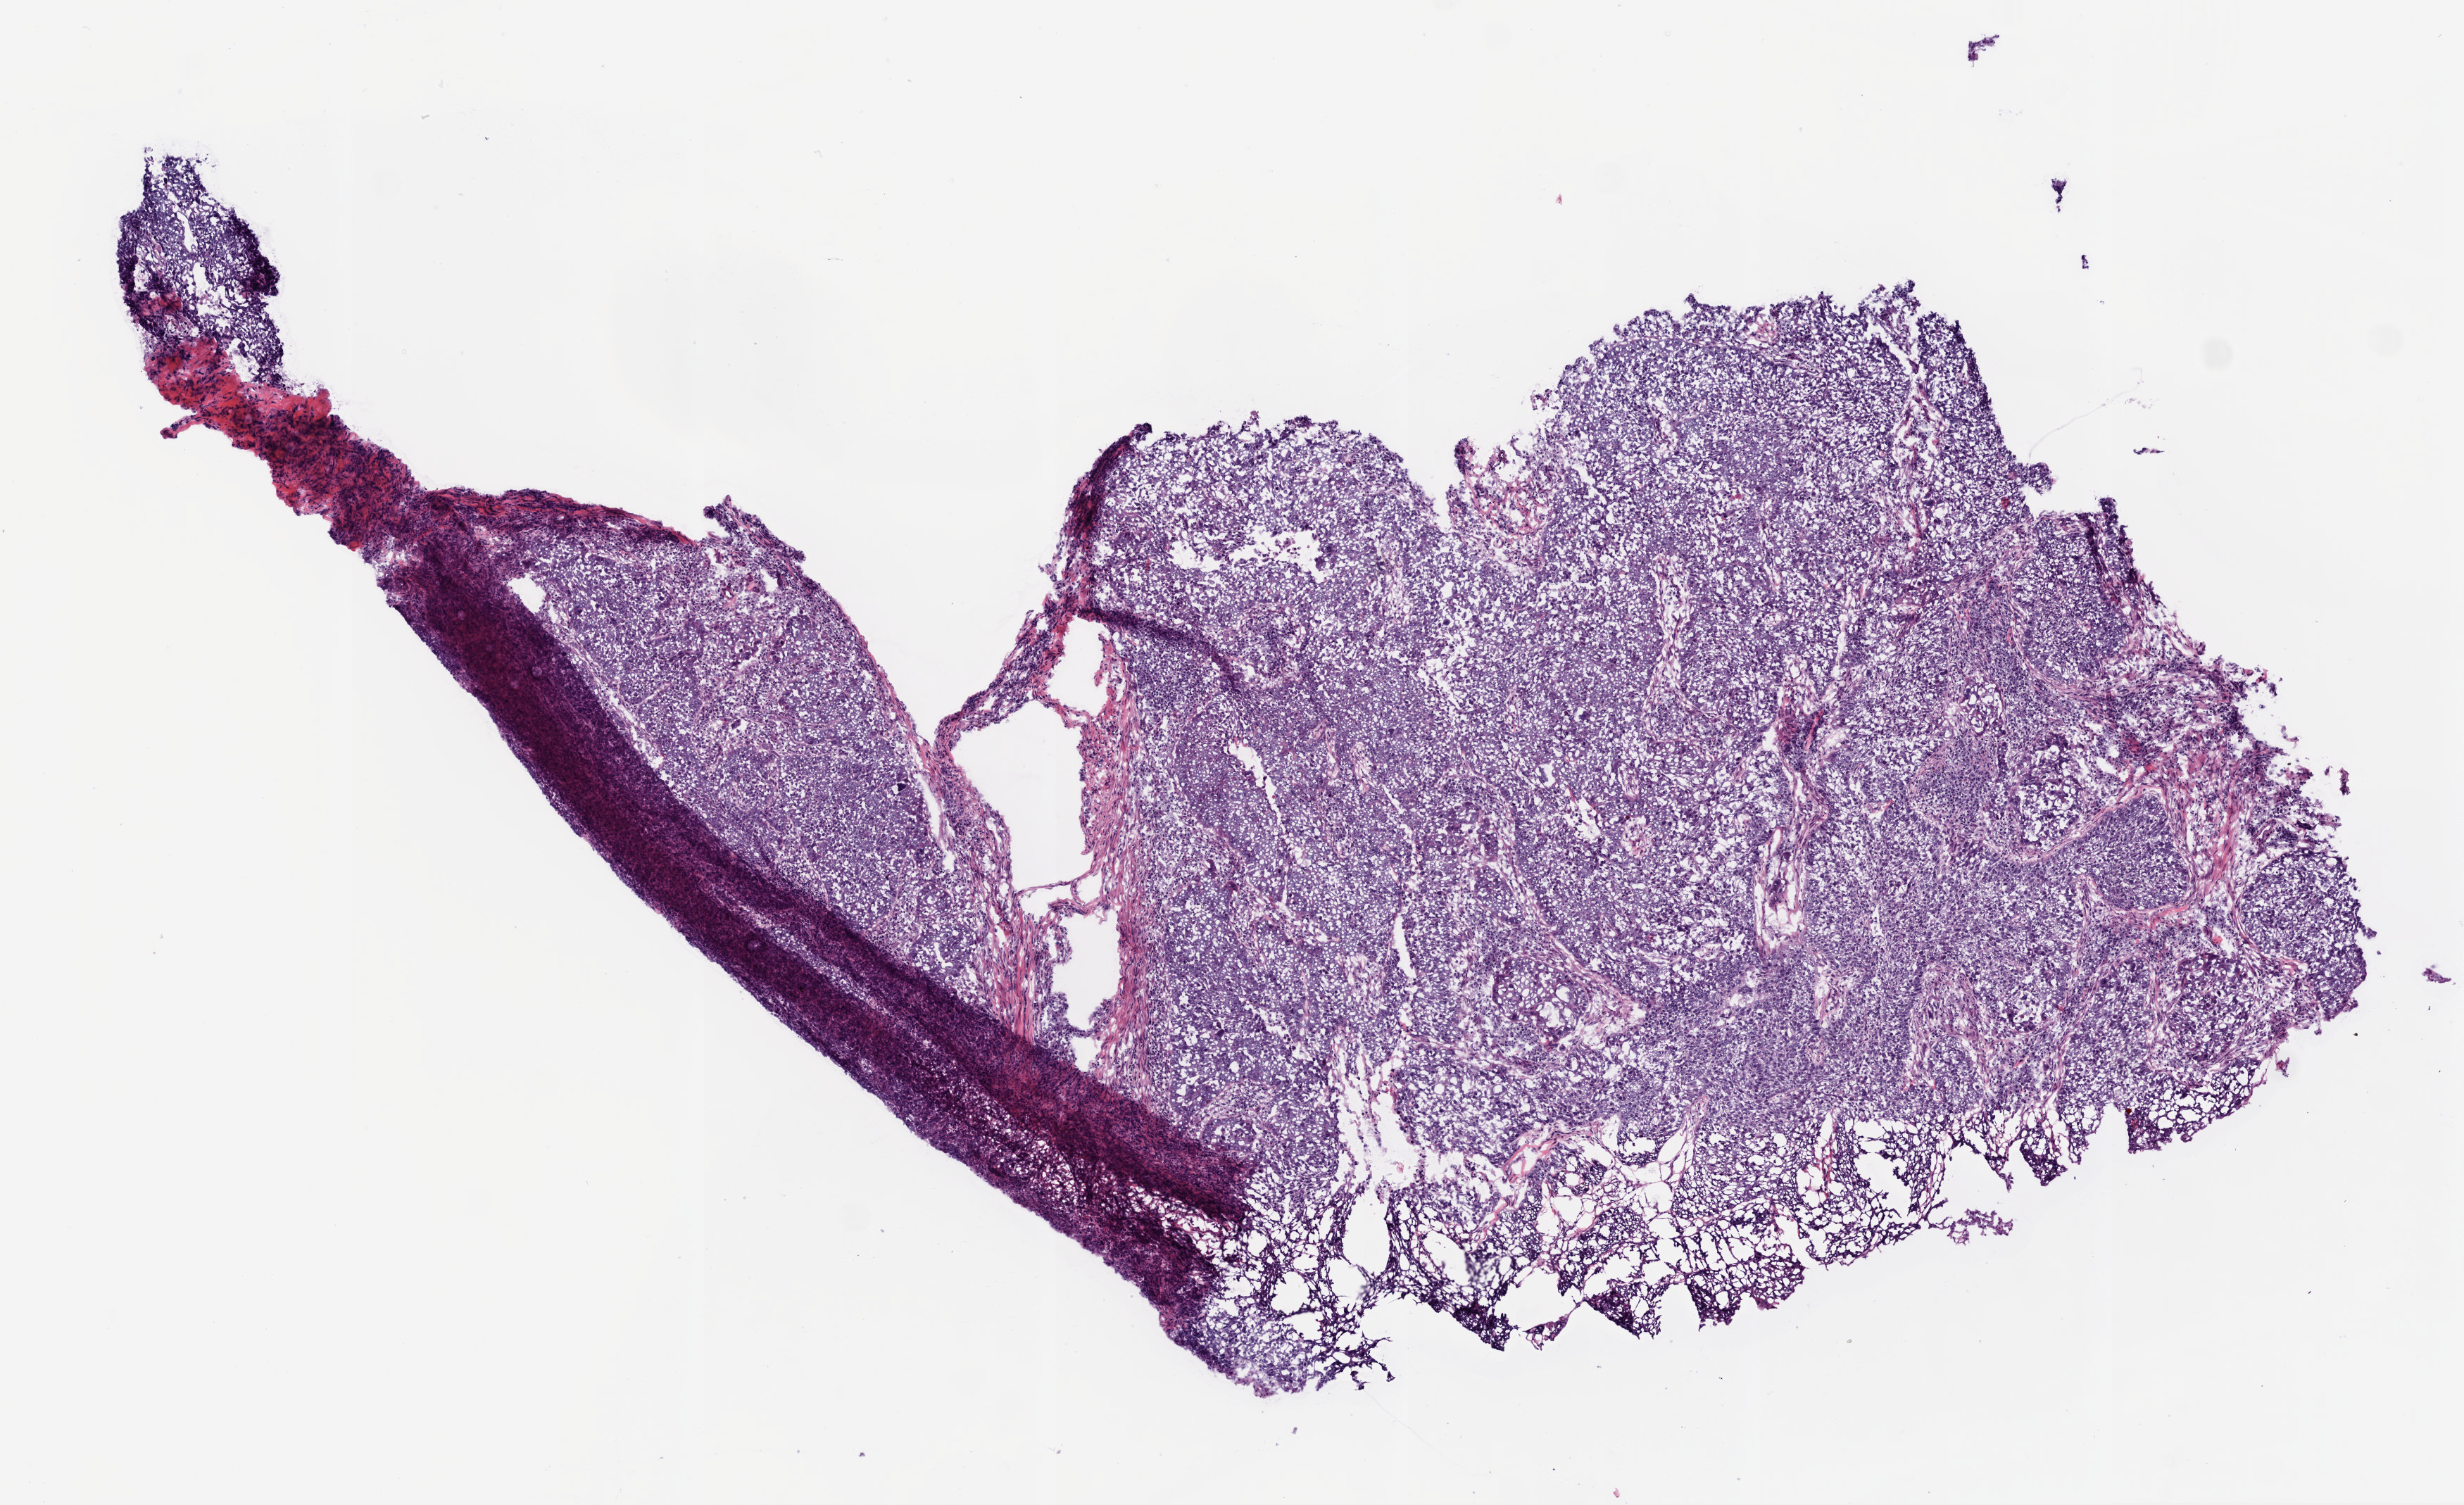
Digitized Hematoxylin and eosin (H&E) stained tissue section (whole slide), a low-resolution overview of the entire scanned area, about 7.0 x 4.3 mm; frozen section from the top of the tissue portion; primary tumour sample from the lung. Female patient; age at initial diagnosis 63 years.
Pathologic diagnosis: Squamous cell carcinoma, NOS.